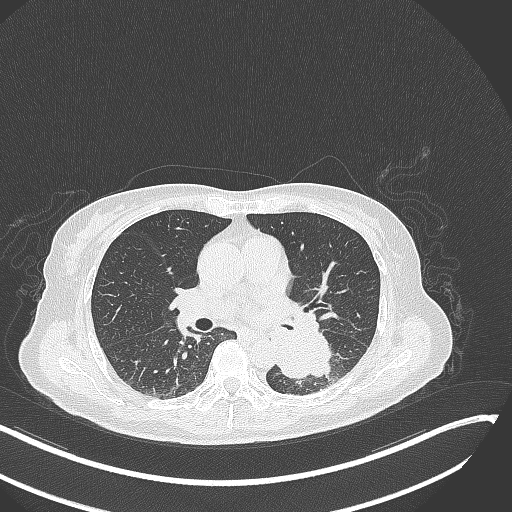
Chest CT, one axial slice. 120 kVp. Lung window (W 1500 / L -600 HU). 1 mm slice thickness. 512 × 512 image matrix, field of view 400 × 400 mm. Female patient, age 64 years. Case-level facts recorded for this patient, not image findings: clinical TNM (as recorded): T3 N1 M1; histopathological grade: G3.
Structures marked on this image (rectangle marked by the reading radiologist):
- lung tumour (recorded histology: small cell carcinoma): bounding box (x1, y1, x2, y2) in pixels: (267, 327, 338, 386)